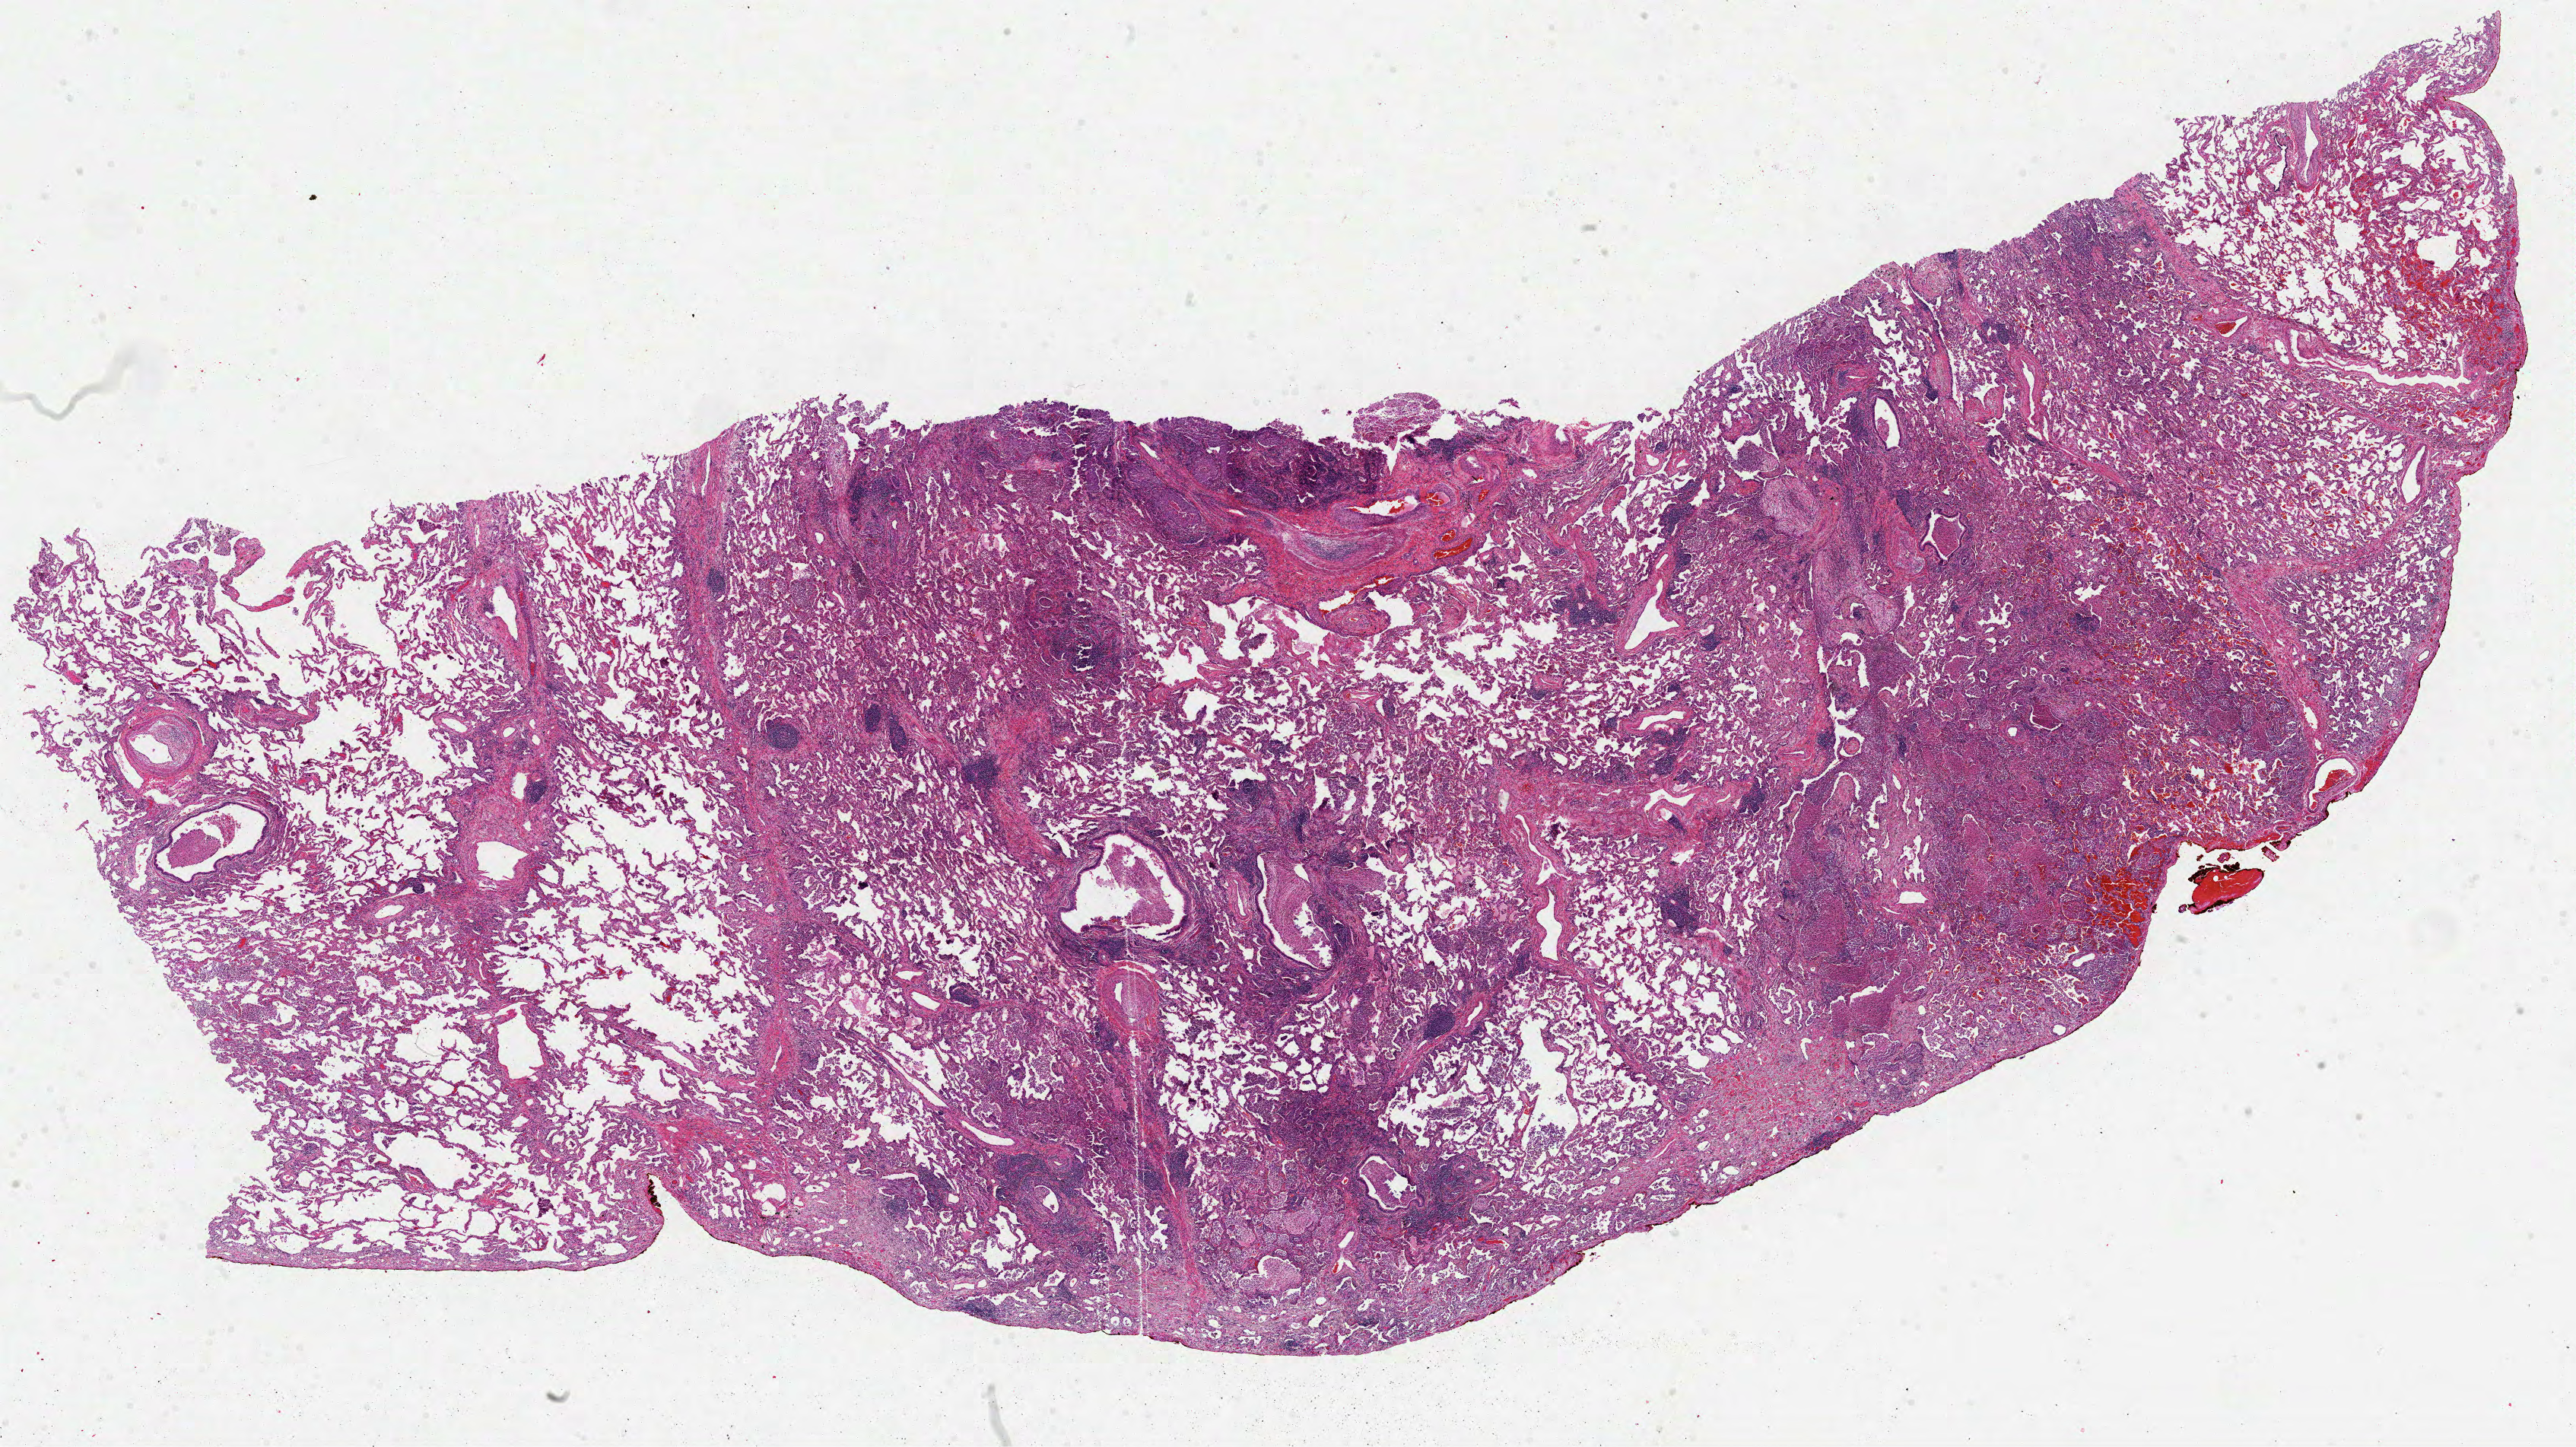
Whole-slide histology image, H&E-stained — whole scanned area (about 27.3 x 15.3 mm, from a 40x scan) shown as a low-resolution overview; formalin-fixed paraffin-embedded (FFPE) diagnostic section; lung, primary tumour sample. Female patient; age at initial diagnosis 81 years.
• AJCC pathologic stage: IIIA
• histologic diagnosis: Clear cell adenocarcinoma, NOS (upper lobe, lung)